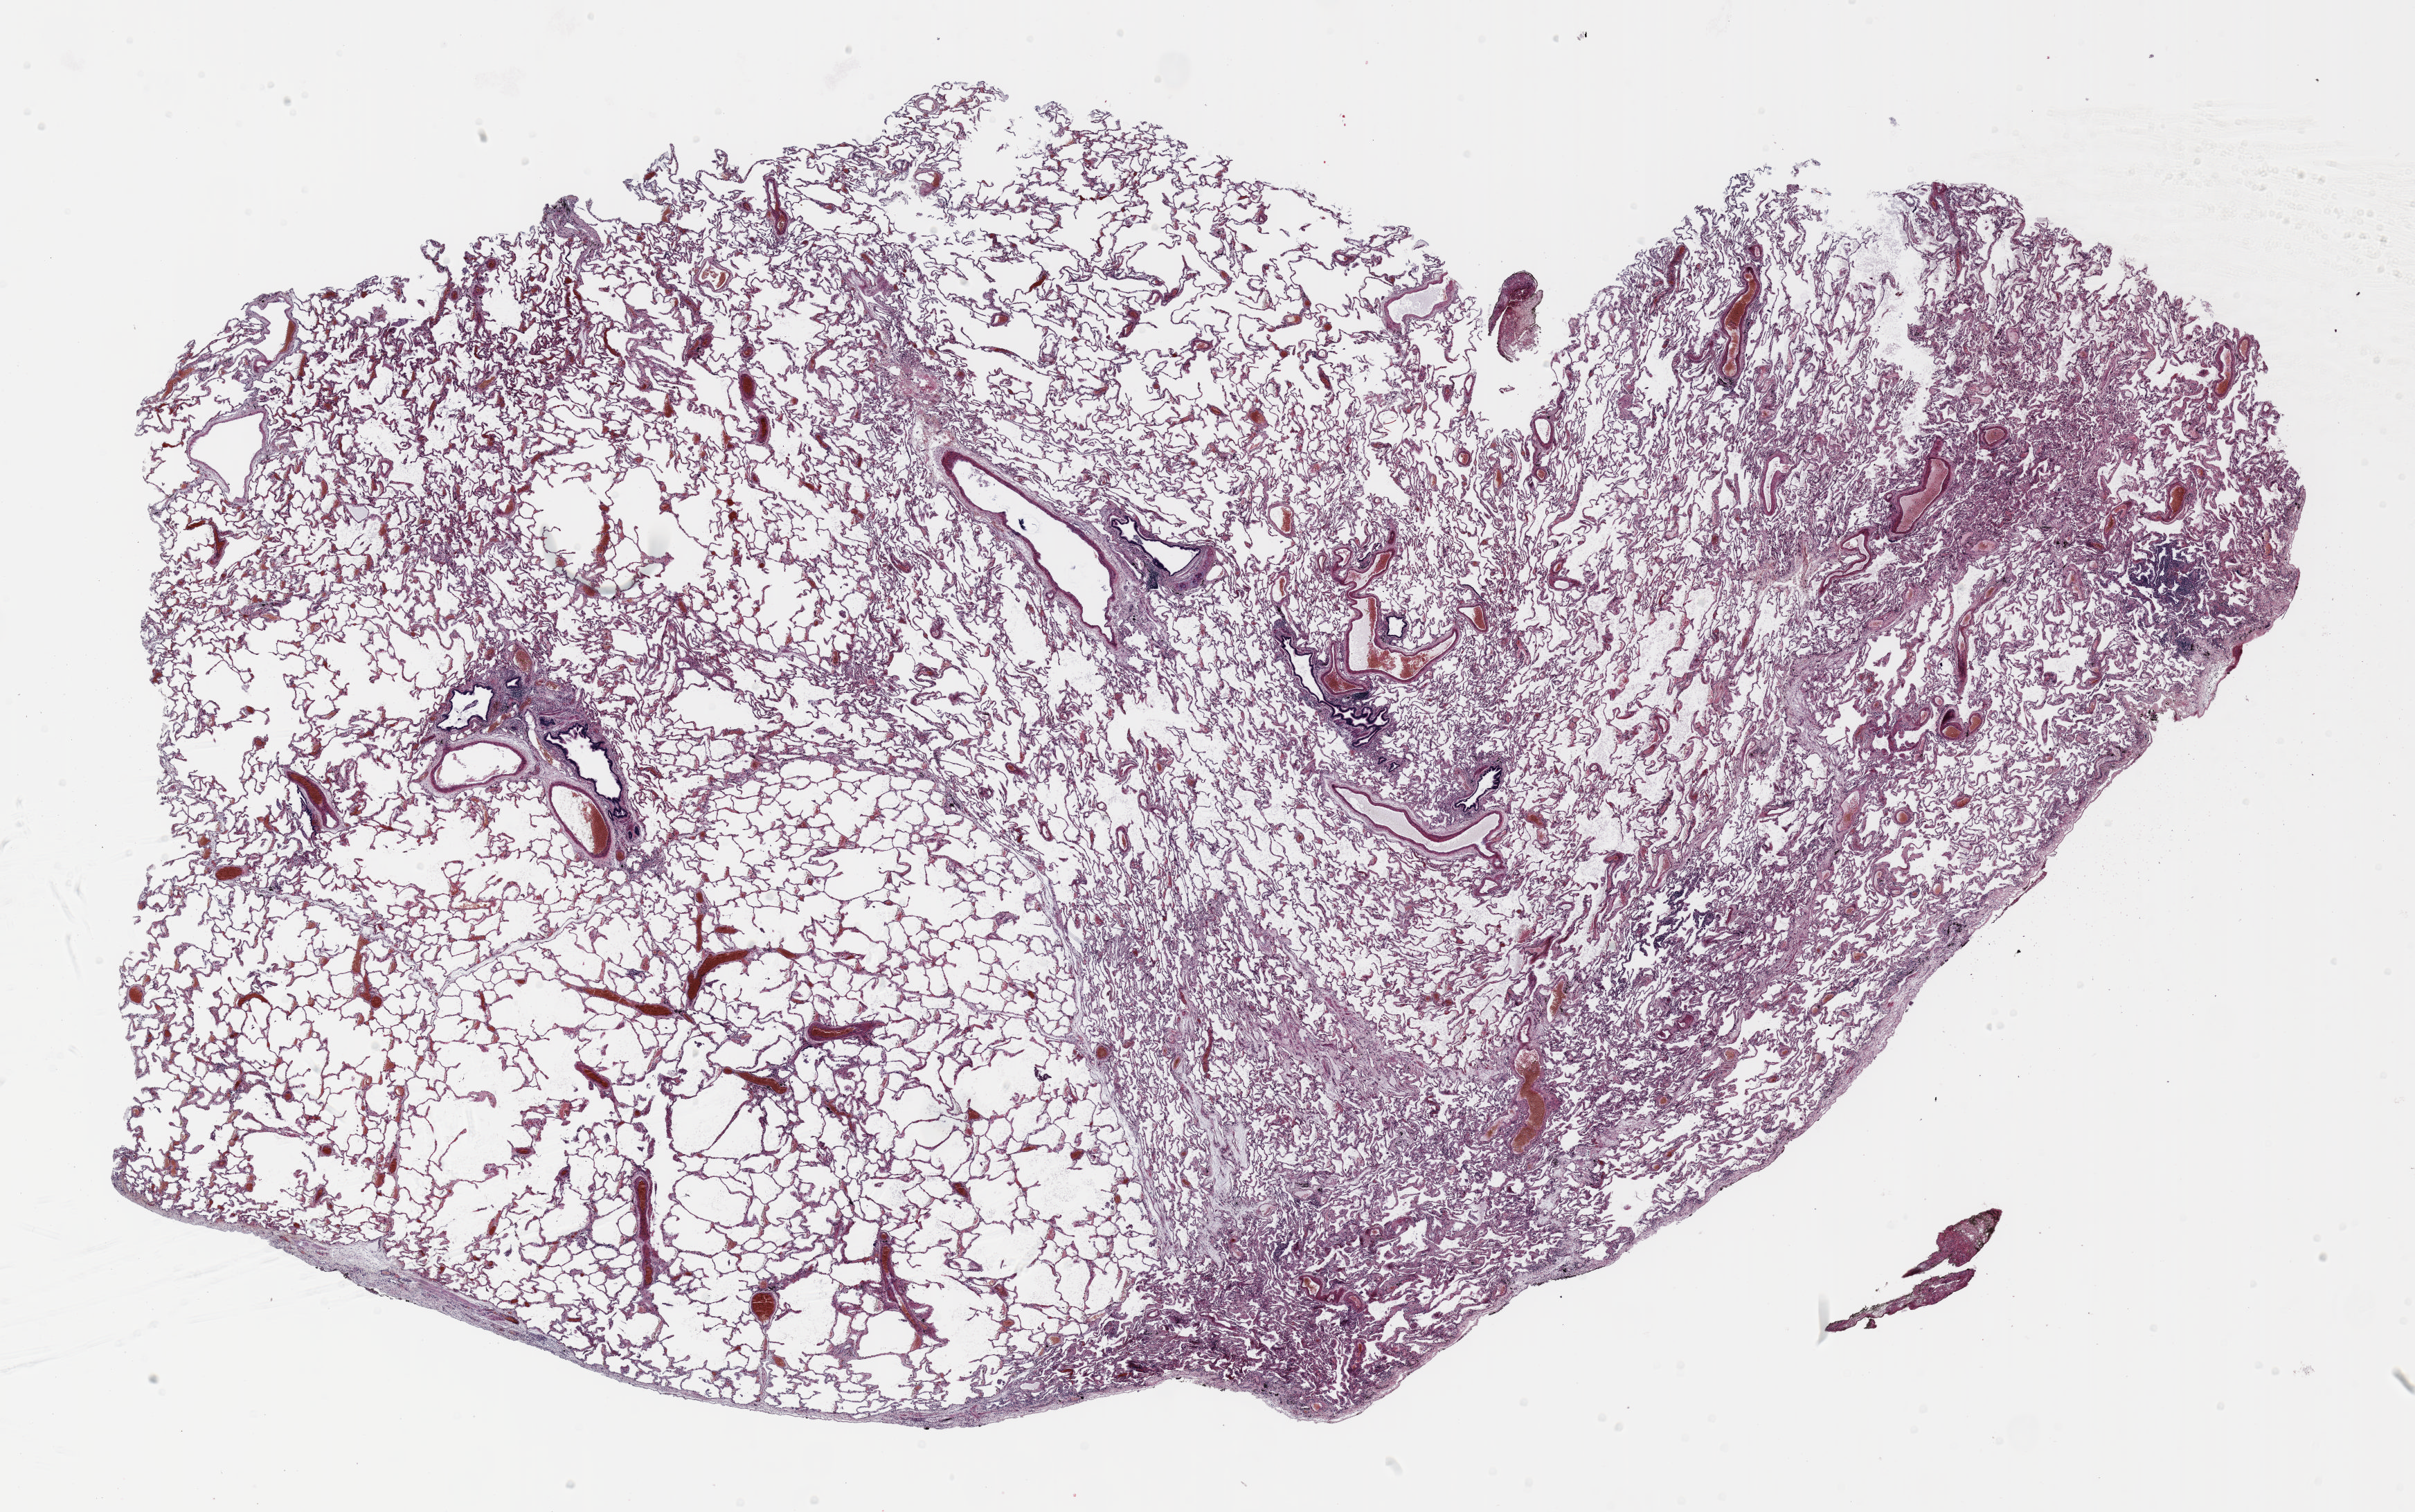
H&E-stained whole-slide image — low-resolution overview of the scanned area, about 28.0 x 17.5 mm; formalin-fixed paraffin-embedded (FFPE) section; lung tissue. Female, age 58 at enrolment. Grade: poorly differentiated (G3).
Tumour size (pathology): 50 mm. Stage (AJCC 6th edition): IIIA. Primary tumour location (clinical record): left lower lobe. Participant's lung-cancer diagnosis: Large cell carcinoma, NOS.